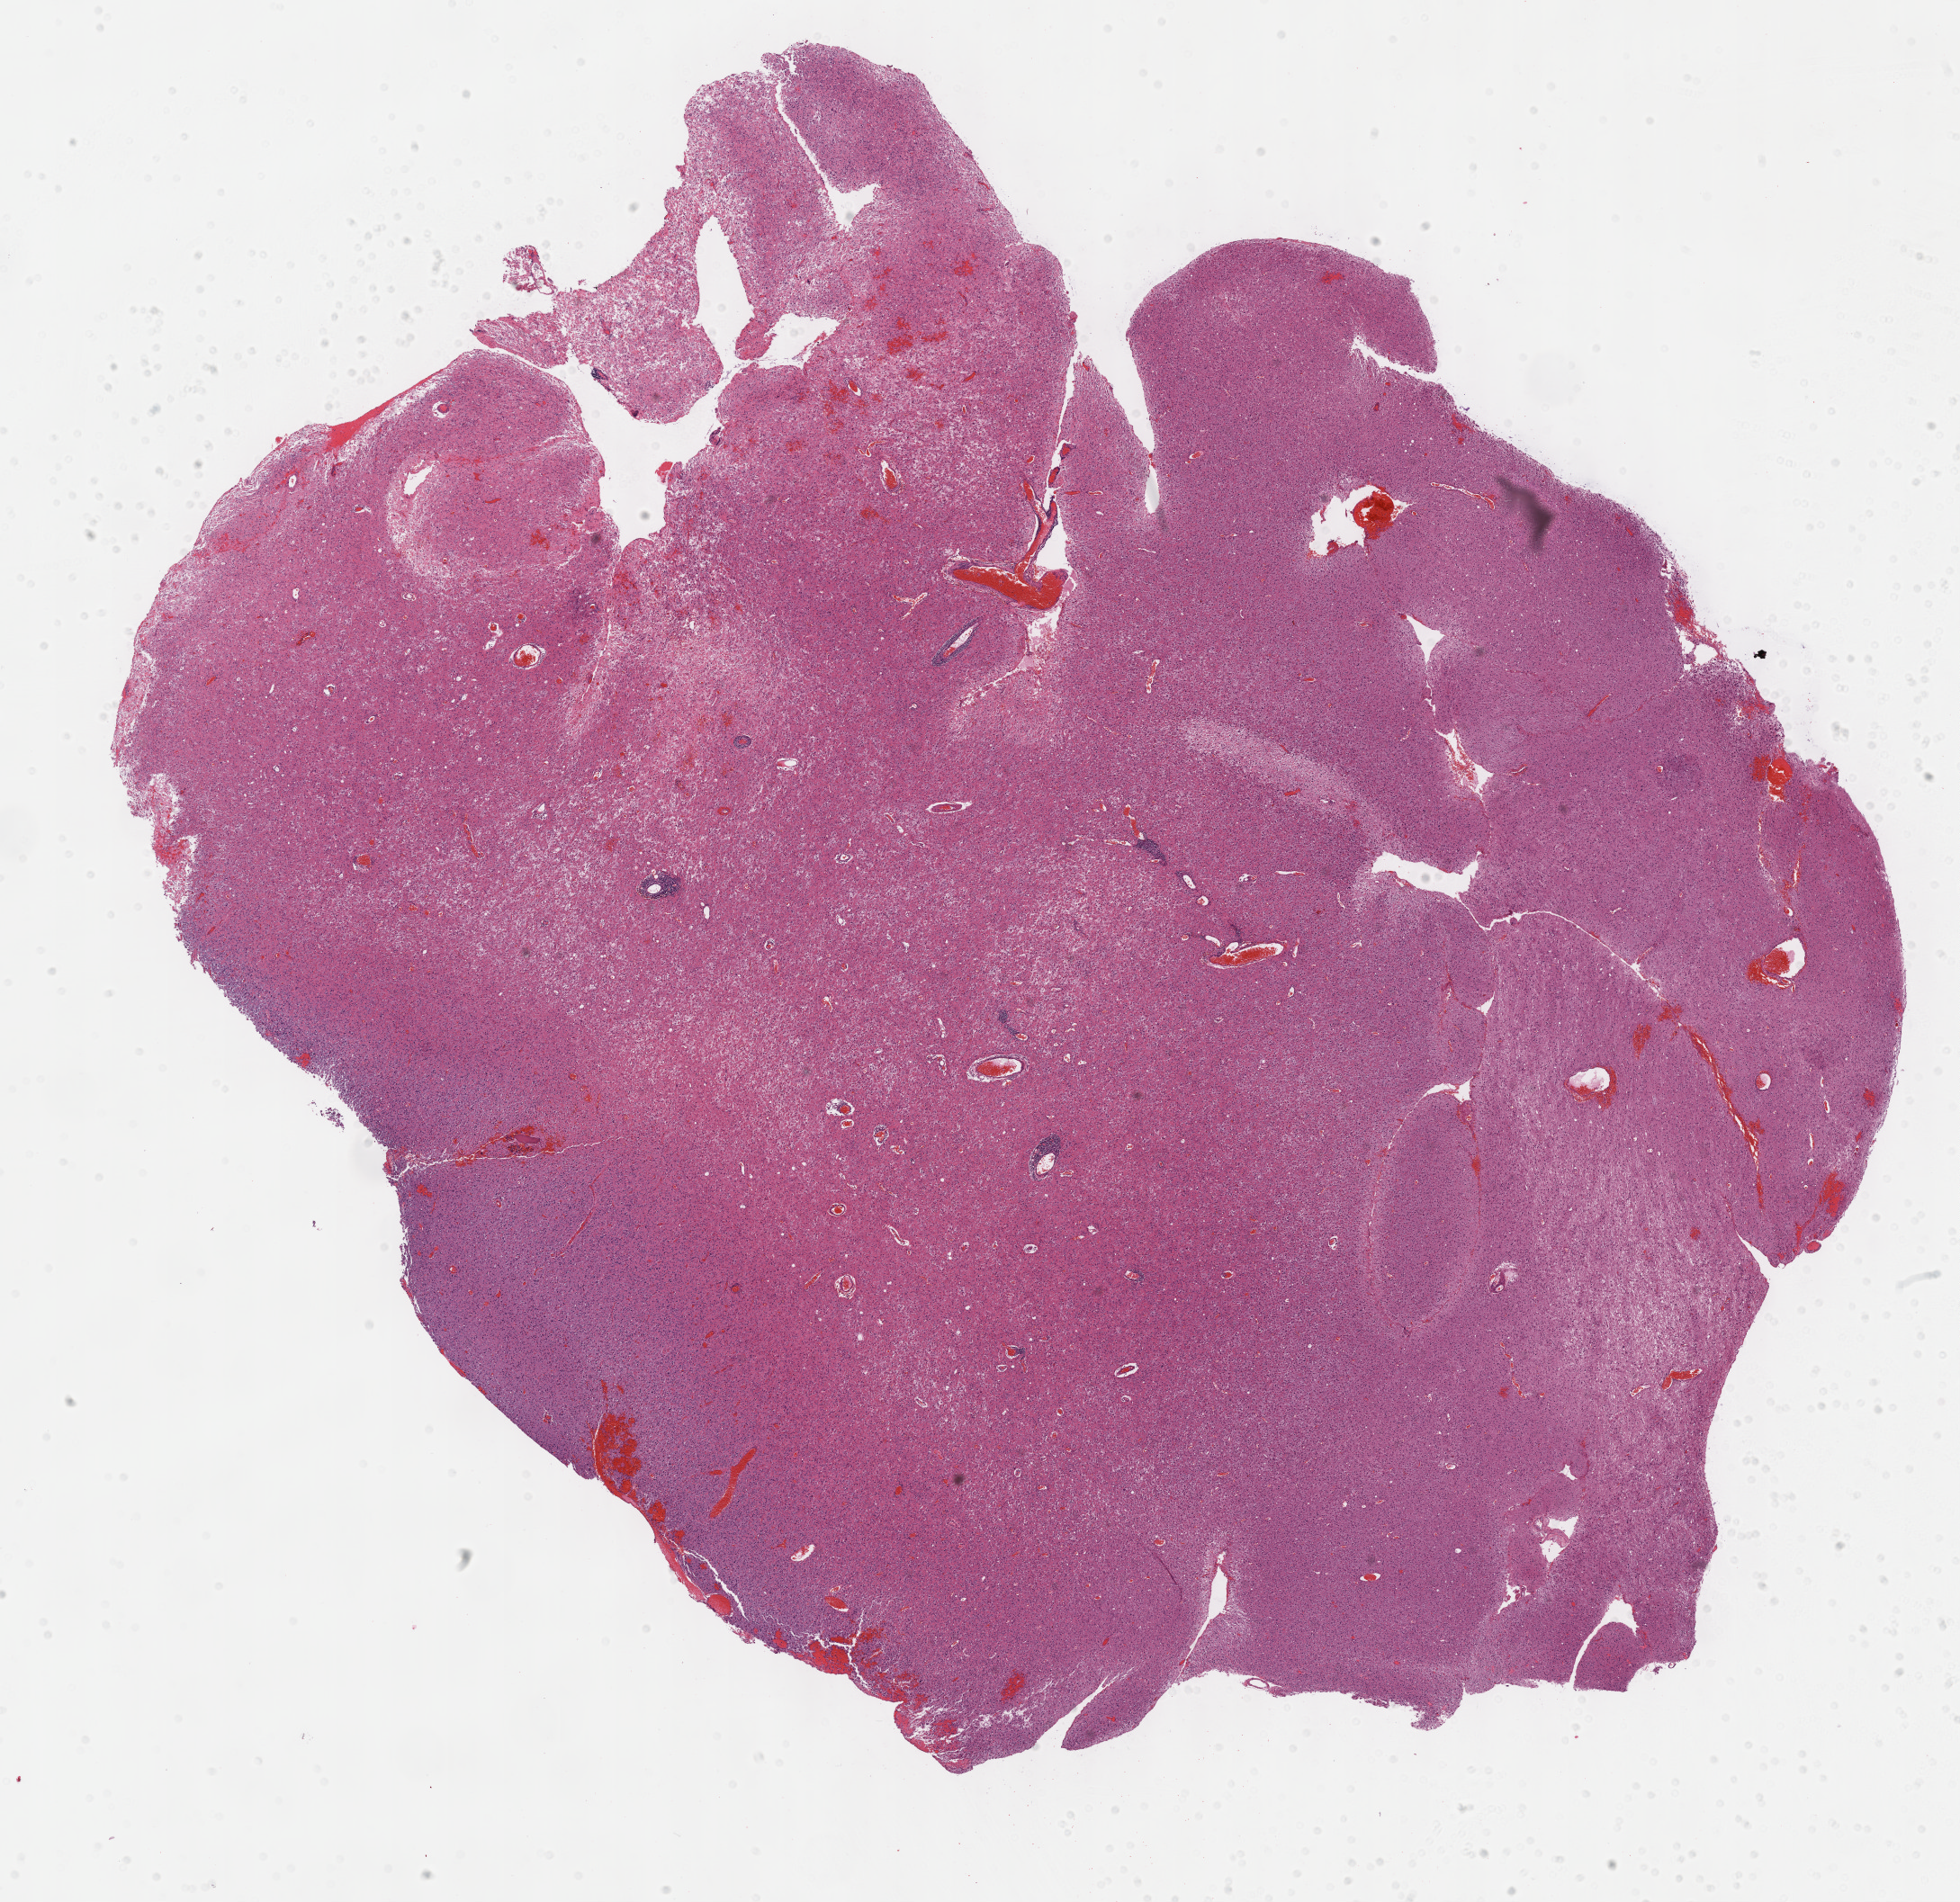
Hematoxylin and eosin (H&E) stained whole-slide image, shown as a low-resolution overview of the whole scanned area (about 17.6 x 17.1 mm, acquisition: 40x scan), formalin-fixed paraffin-embedded (FFPE) diagnostic section, sample: primary tumour, brain. Patient: male, age at initial diagnosis 37 years. Histologic grade: G3 (poorly differentiated).
Pathologic diagnosis: Oligodendroglioma, anaplastic.